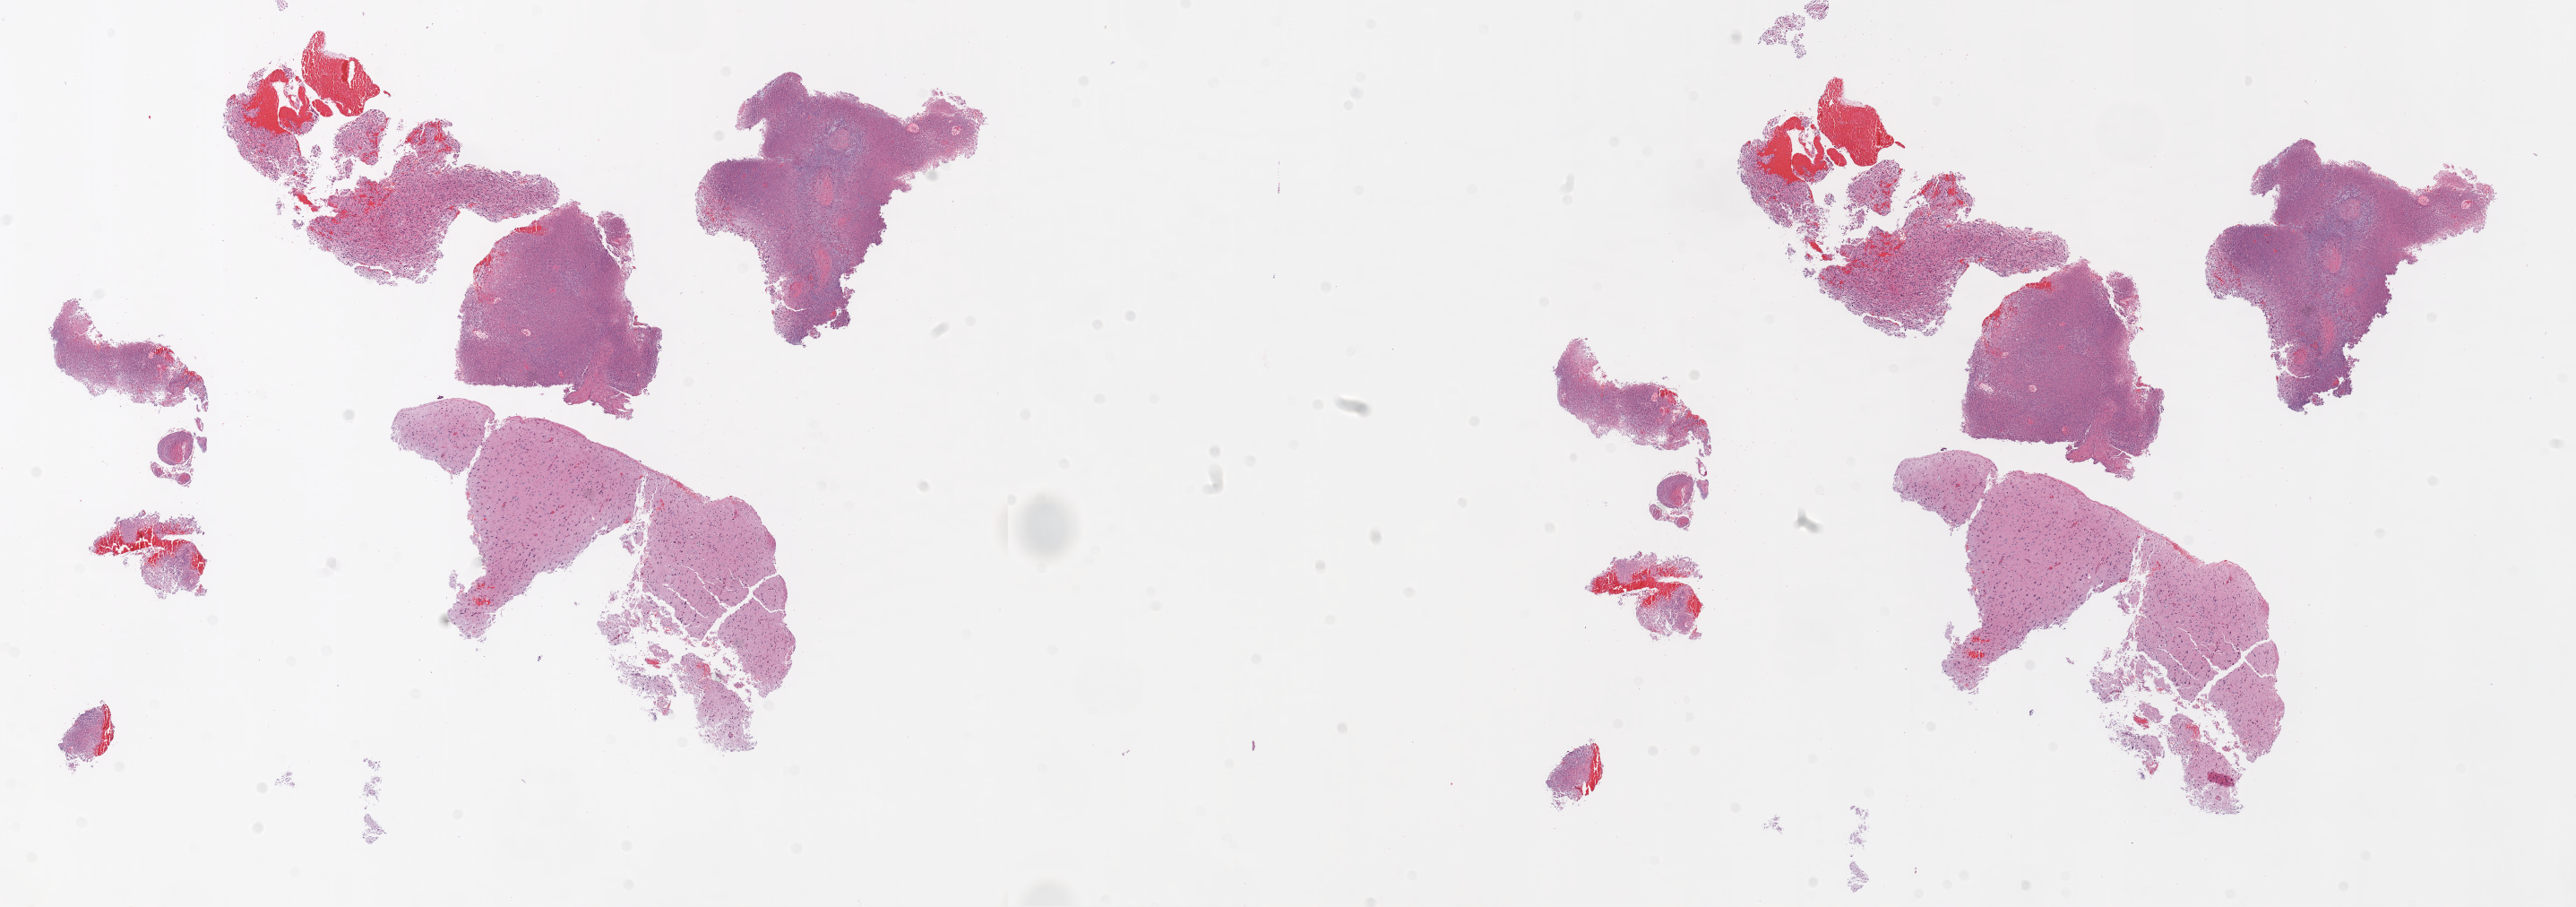
H&E whole-slide image — a low-resolution overview of the entire scanned area, about 23.1 x 8.1 mm (slide scanned at 20x), formalin-fixed paraffin-embedded (FFPE) diagnostic section, primary tumour sample from the brain. Female, age 73 years at initial diagnosis.
Histologic diagnosis: Glioblastoma.